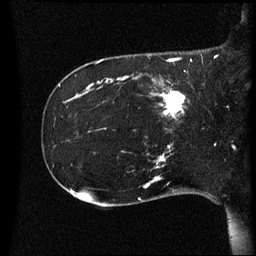
Breast MRI (dynamic contrast-enhanced), one sagittal slice. Dynamic contrast-enhanced series, image 2 of 3 at this slice position (ordered by acquisition). 1.5 T. TE 4.2 ms, TR 8.4 ms. 2.2 mm slice thickness. 256 × 256 image matrix, field of view 220 × 220 mm. Female patient, age 41 years. From the clinical record (not read from this slice): setting: breast cancer imaged before/during neoadjuvant chemotherapy; receptor status: HER2-positive.
Outlined on this slice (semi-automatically segmented with operator editing):
- analysis volume of interest (the breast-tissue region the enhancement analysis was run in; not a lesion): bounding box [x1, y1, x2, y2] px = [122, 80, 195, 125]
- tumour enhancement mask (voxels above the 70 % enhancement threshold inside the analysis volume of interest): [159, 88, 186, 119]